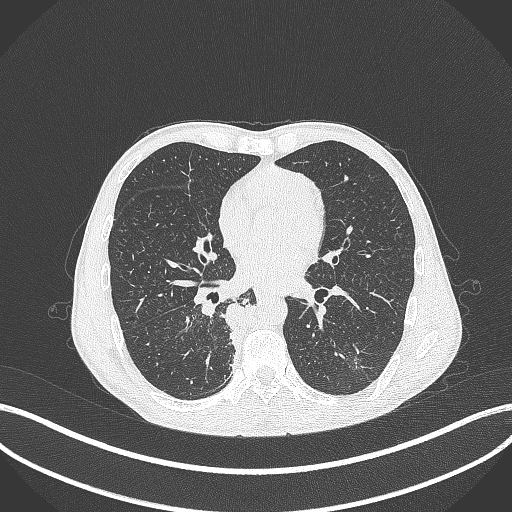
Chest CT, one axial slice. Slice 176 of 371 in the series (ordered by position). Reconstruction kernel B70f. 120 kVp. Lung window (W 1500 / L -600 HU). 1 mm slice thickness. 512 × 512 image matrix, field of view 400 × 400 mm. Patient: male, 58 years. From the clinical record (not read from this slice): clinical TNM (as recorded): T3 N1 M1.
Structures marked on this image (bounding box drawn by a radiologist):
- lung tumour (recorded histology: squamous cell carcinoma): bounding box [x1, y1, x2, y2] px = [217, 293, 265, 366]